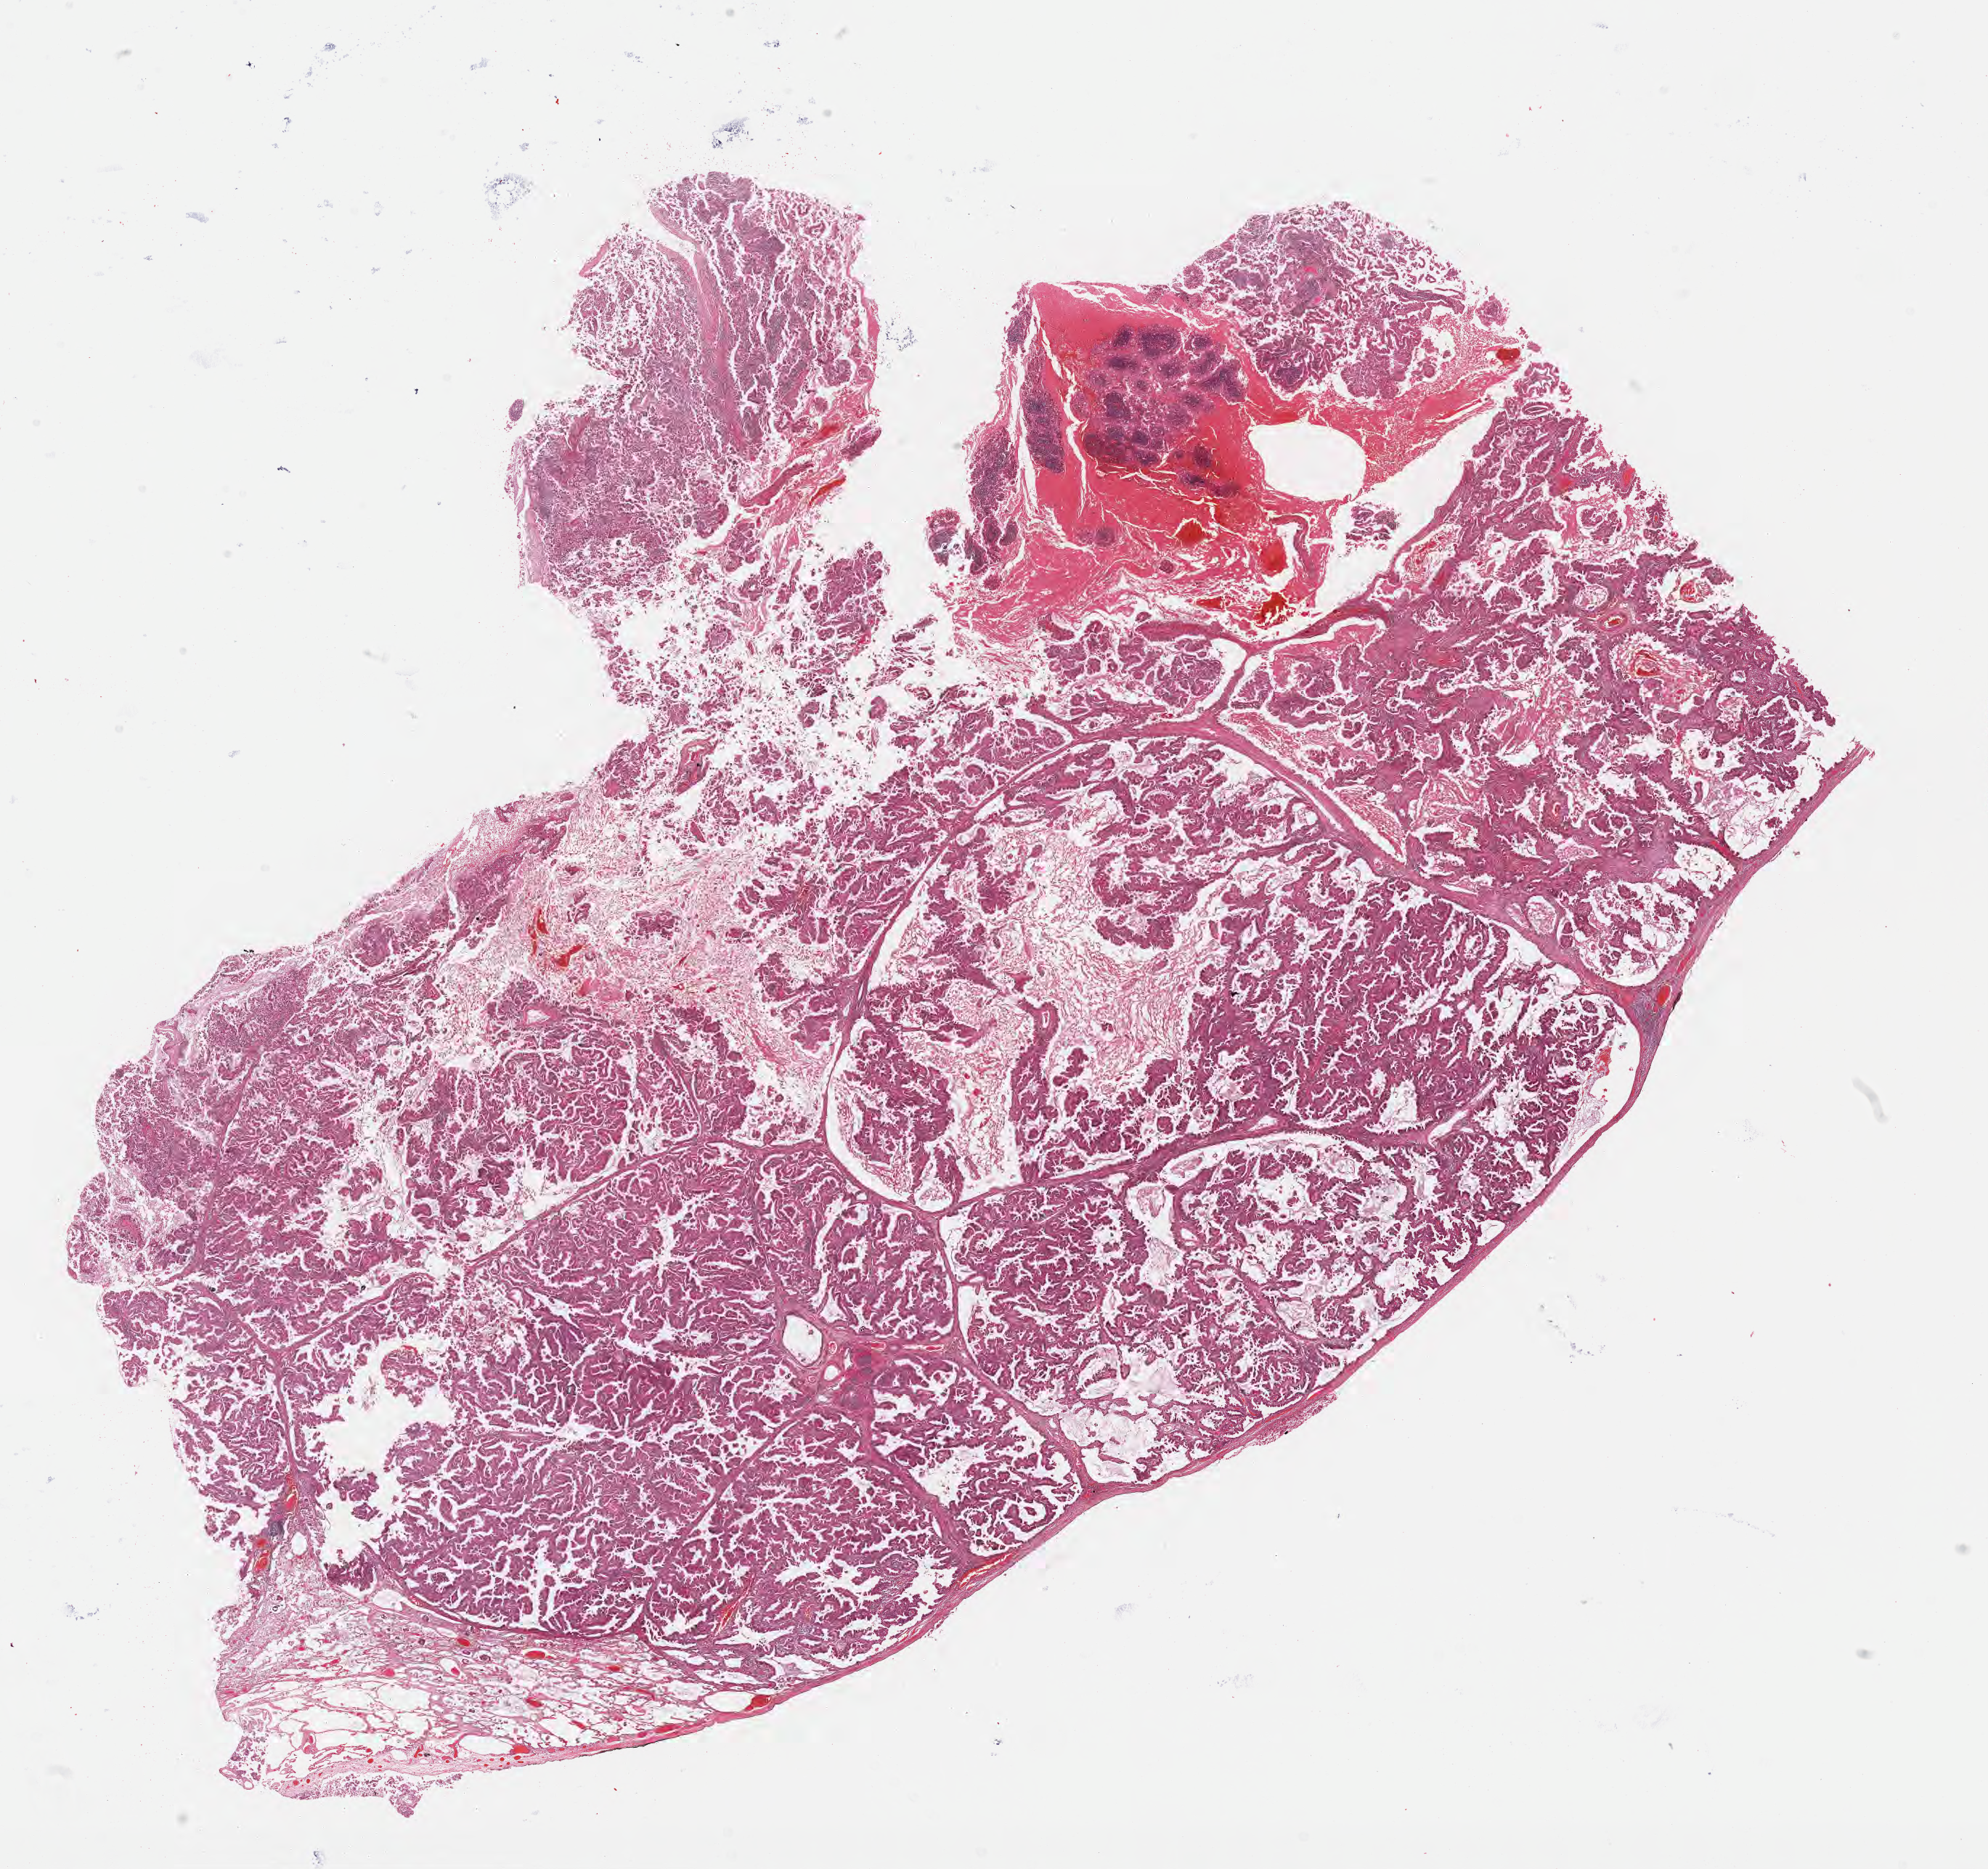
Haematoxylin and eosin whole-slide image, a low-resolution overview of the entire scanned area, about 22.1 x 20.8 mm, FFPE section, primary tumor, anatomic site: lower lobe of left lung. Patient female; age 62 years. Slide review estimates, as recorded: tumor cells 80%, tumor nuclei 85%, stromal cells 10%, necrosis 5%, normal cells 5%. Infiltration values recorded for this section: lymphocyte infiltration 0%, monocyte infiltration 0%, neutrophil infiltration 0%.
Diagnosis: Adenocarcinoma with mixed subtypes. AJCC pathologic stage: Stage IIIA.